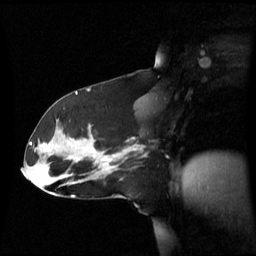
Breast MRI (dynamic contrast-enhanced), one sagittal slice; slice 34 of 60 in the series (ordered by position); dynamic contrast-enhanced series, image 2 of 3 at this slice position (ordered by acquisition); 1.5 T; TE 4.2 ms, TR 8.4 ms; 256 × 256 image matrix, field of view 270 × 270 mm. Female patient, age 39 years. Case-level facts recorded for this patient, not image findings: setting: breast cancer imaged before/during neoadjuvant chemotherapy; receptor status: triple-negative.
Annotated regions visible in this slice (semi-automatically segmented with operator editing):
- analysis volume of interest (the breast-tissue region the enhancement analysis was run in; not a lesion): bounding box <101,137,146,173> (left, top, right, bottom; pixels)
- tumour enhancement mask (voxels above the 70 % enhancement threshold inside the analysis volume of interest): <101,148,135,160>